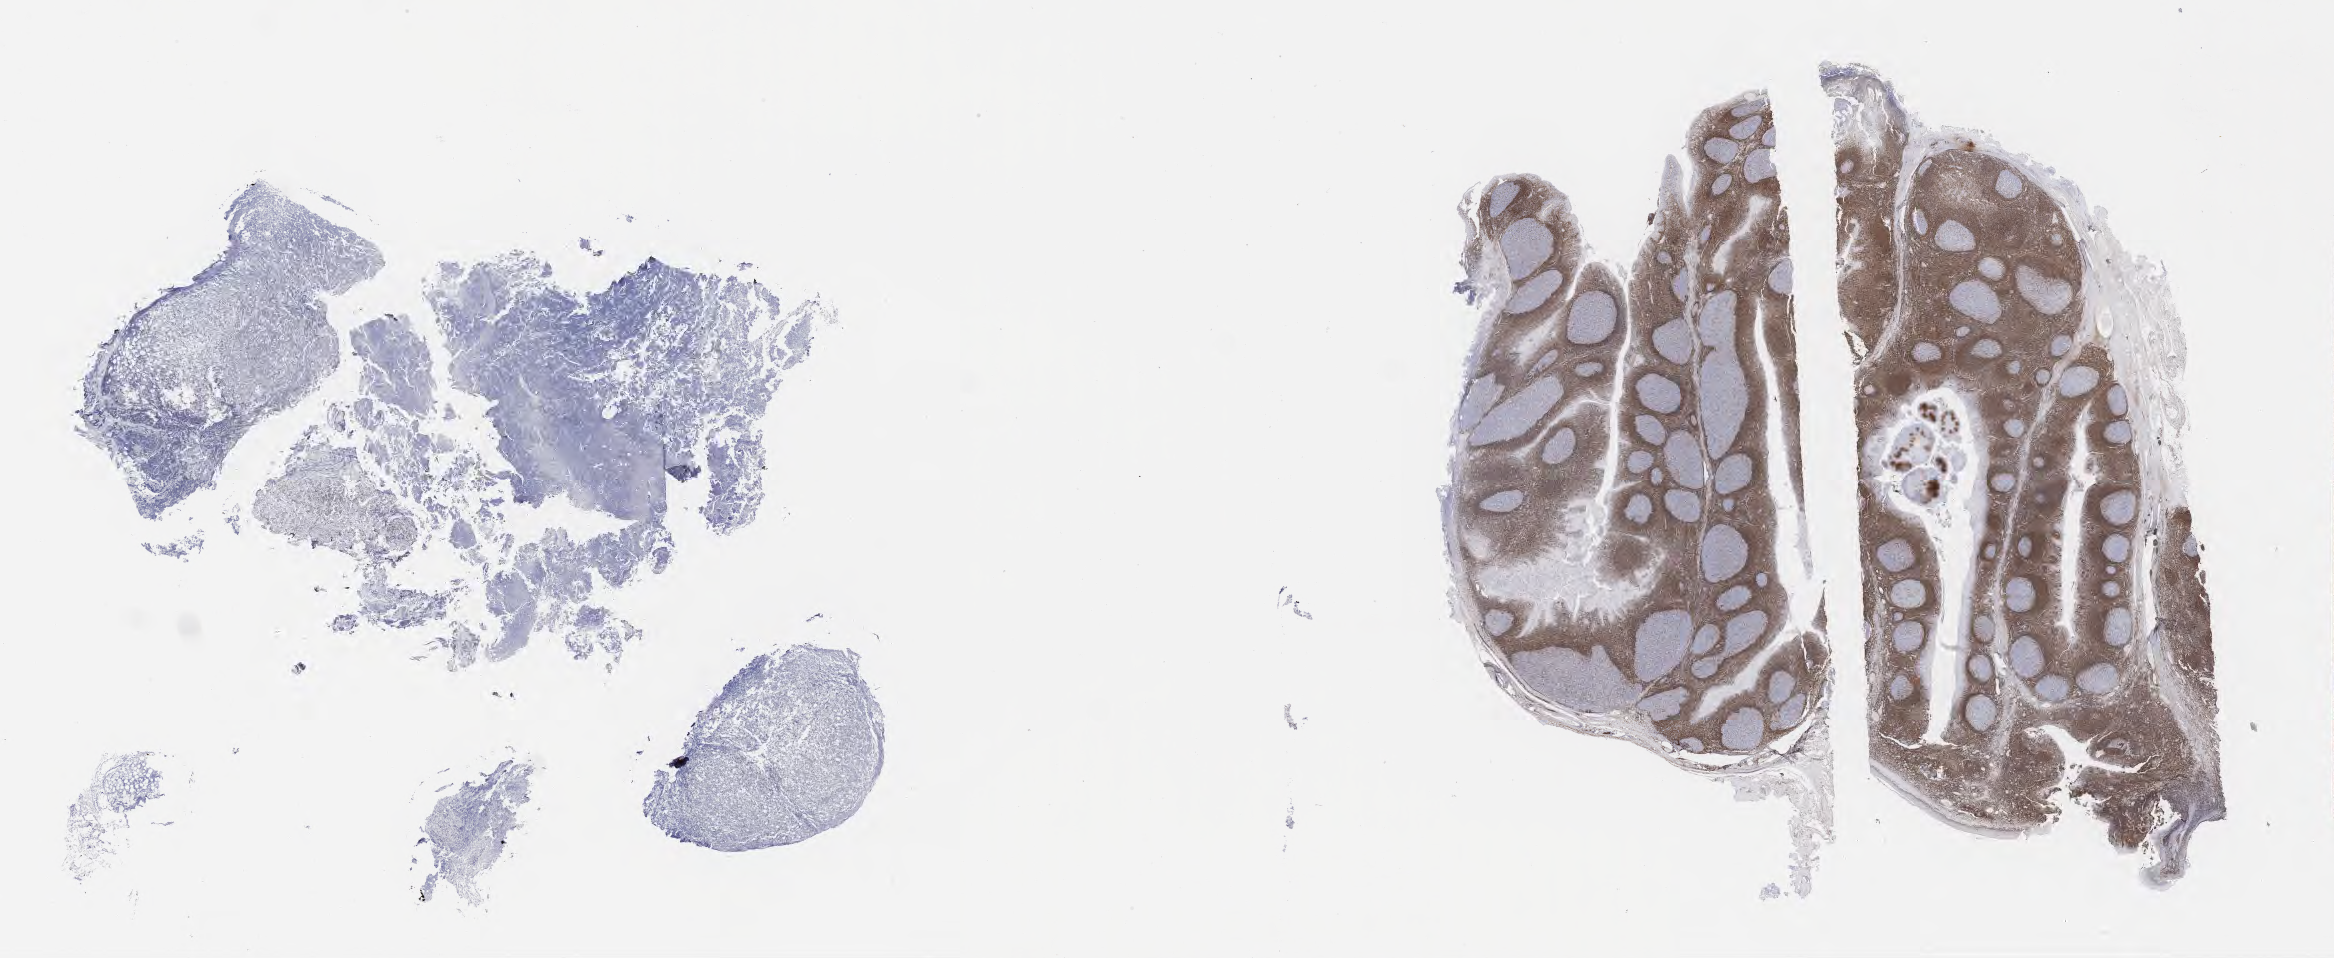
Whole-slide image, immunohistochemical stain for BCL2 — shown as a low-resolution overview of the whole scanned area (about 37.7 x 15.5 mm). Specimen: tumor tissue. Male patient, aged 23.
Histologic diagnosis: Burkitt lymphoma, NOS.